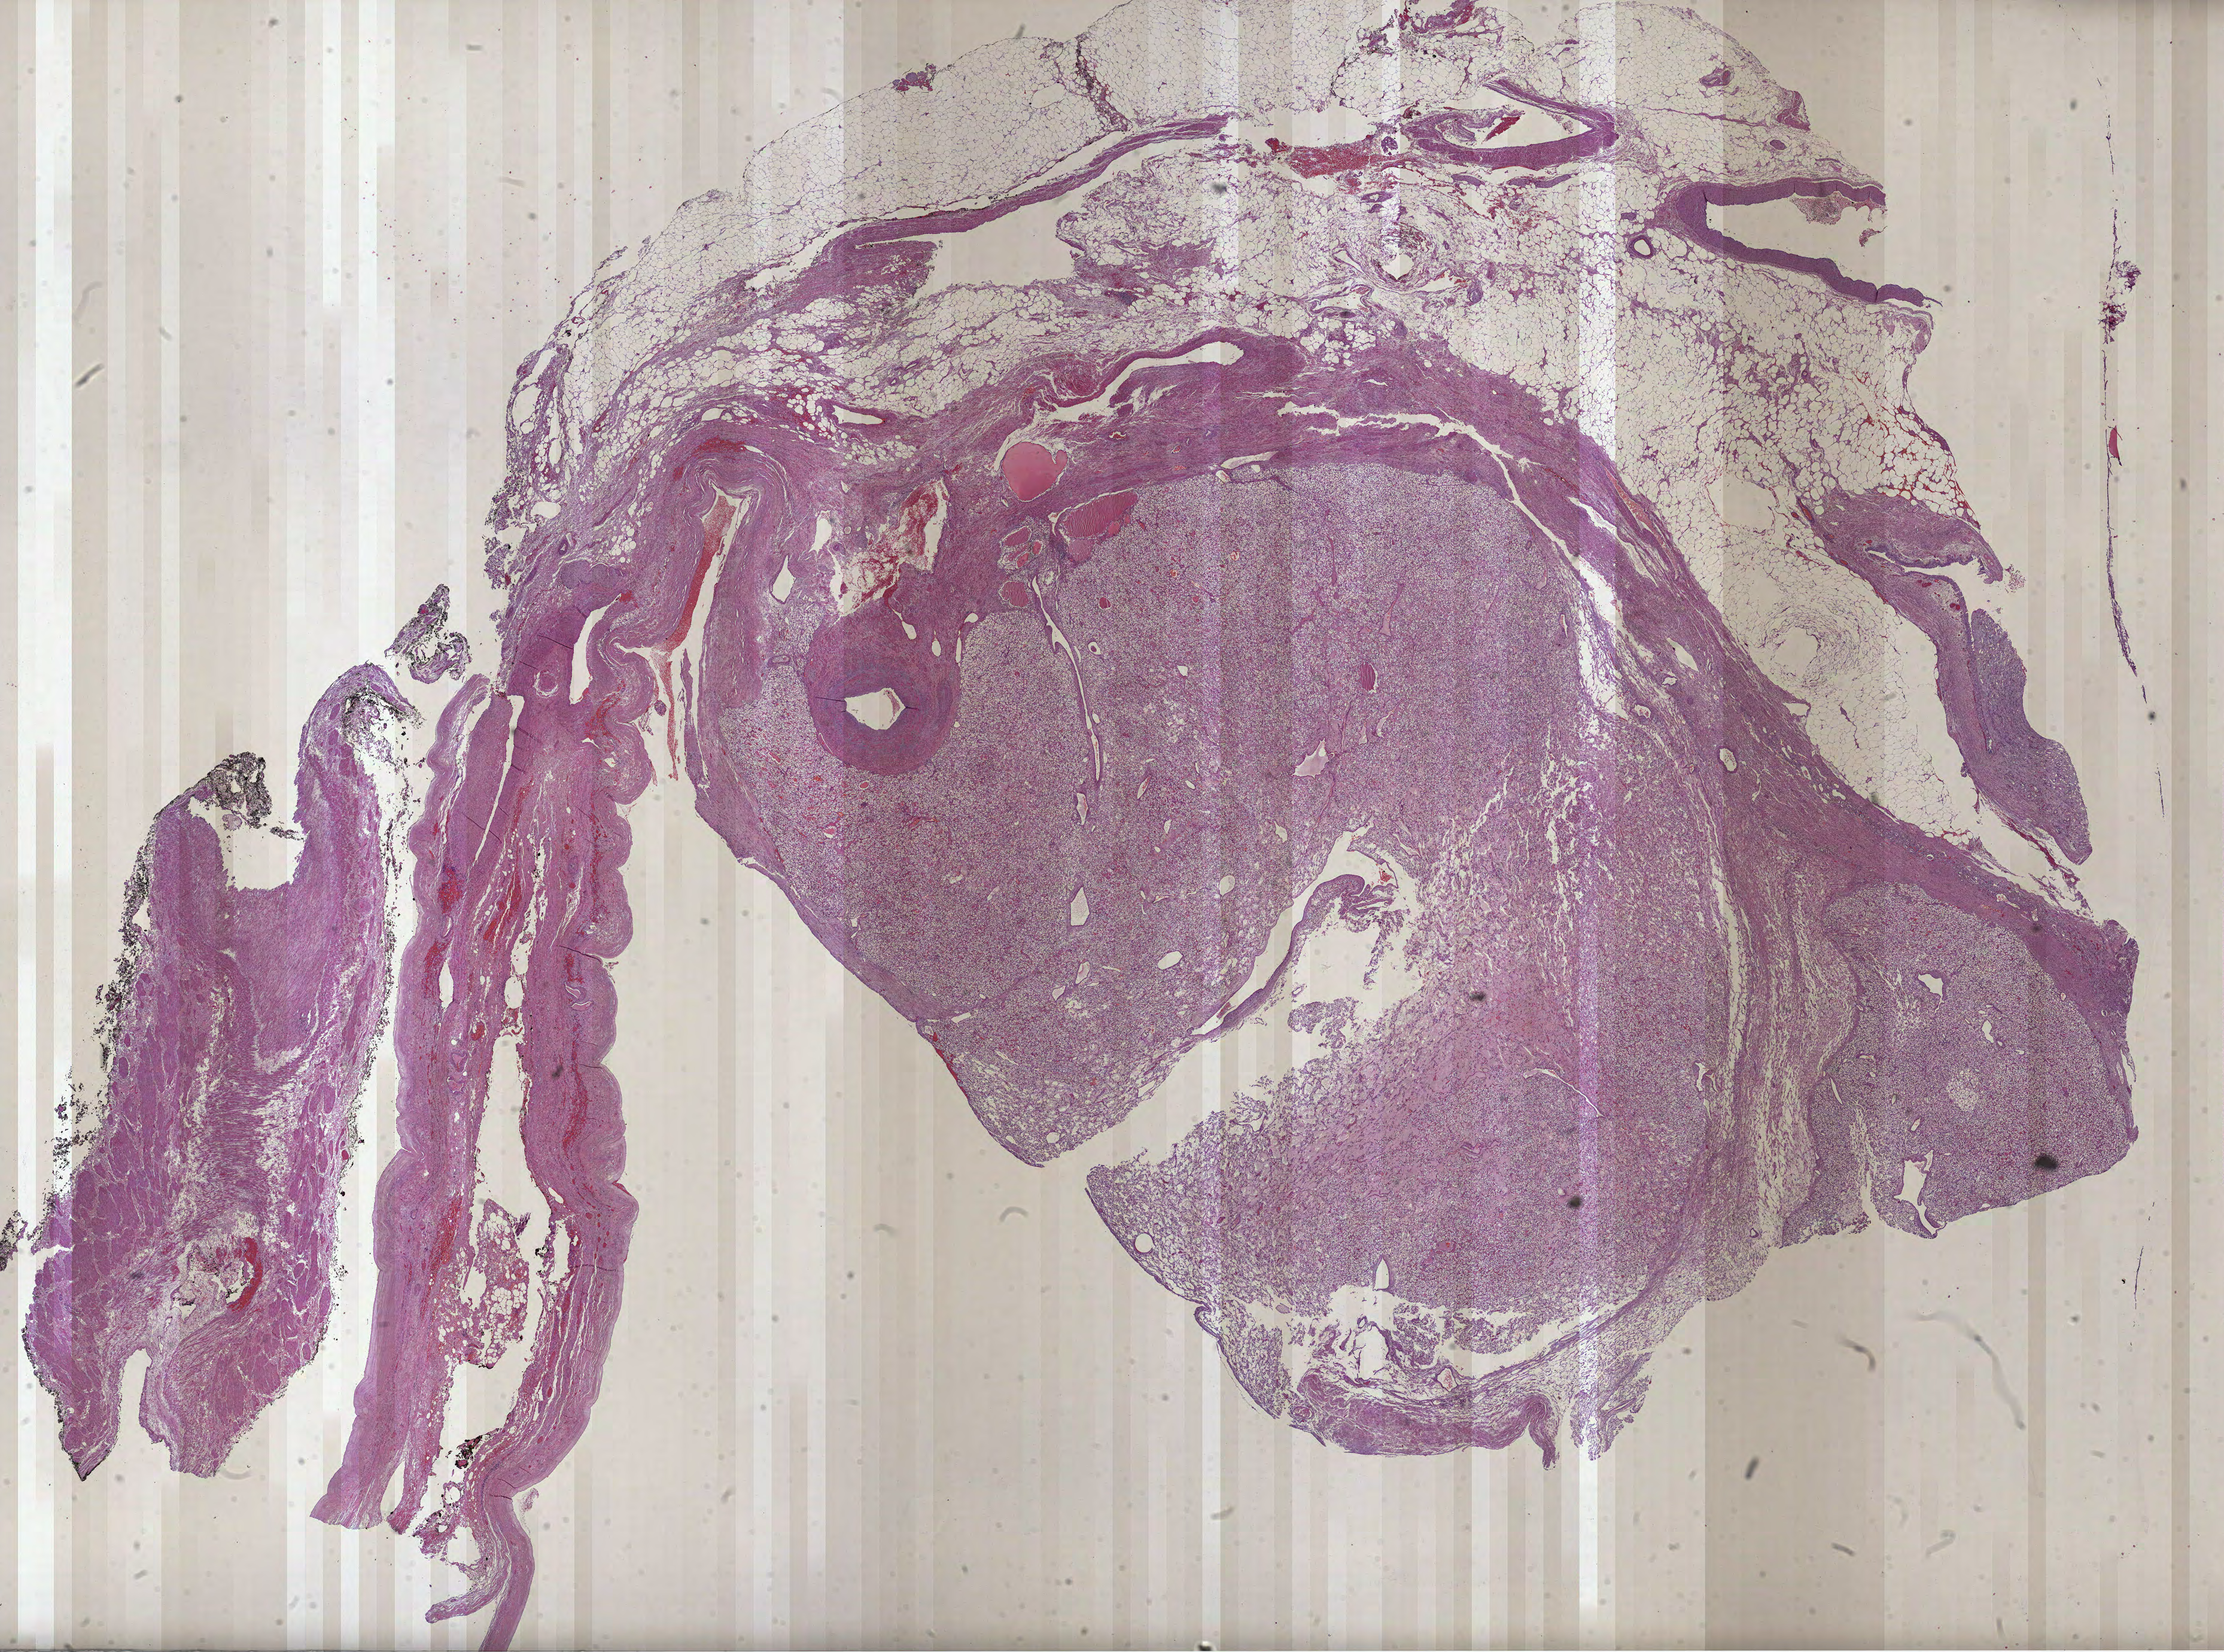
Whole-slide histology image, Hematoxylin and eosin (H&E) stained — shown as a low-resolution overview of the whole scanned area (about 30.0 x 22.3 mm), formalin-fixed paraffin-embedded (FFPE) diagnostic section, sample: primary tumour, kidney. Female, age 57 years at initial diagnosis. Histologic grade: G1 (well differentiated).
Pathologic diagnosis: Renal cell carcinoma, NOS. AJCC pathologic stage: I (7th edition).